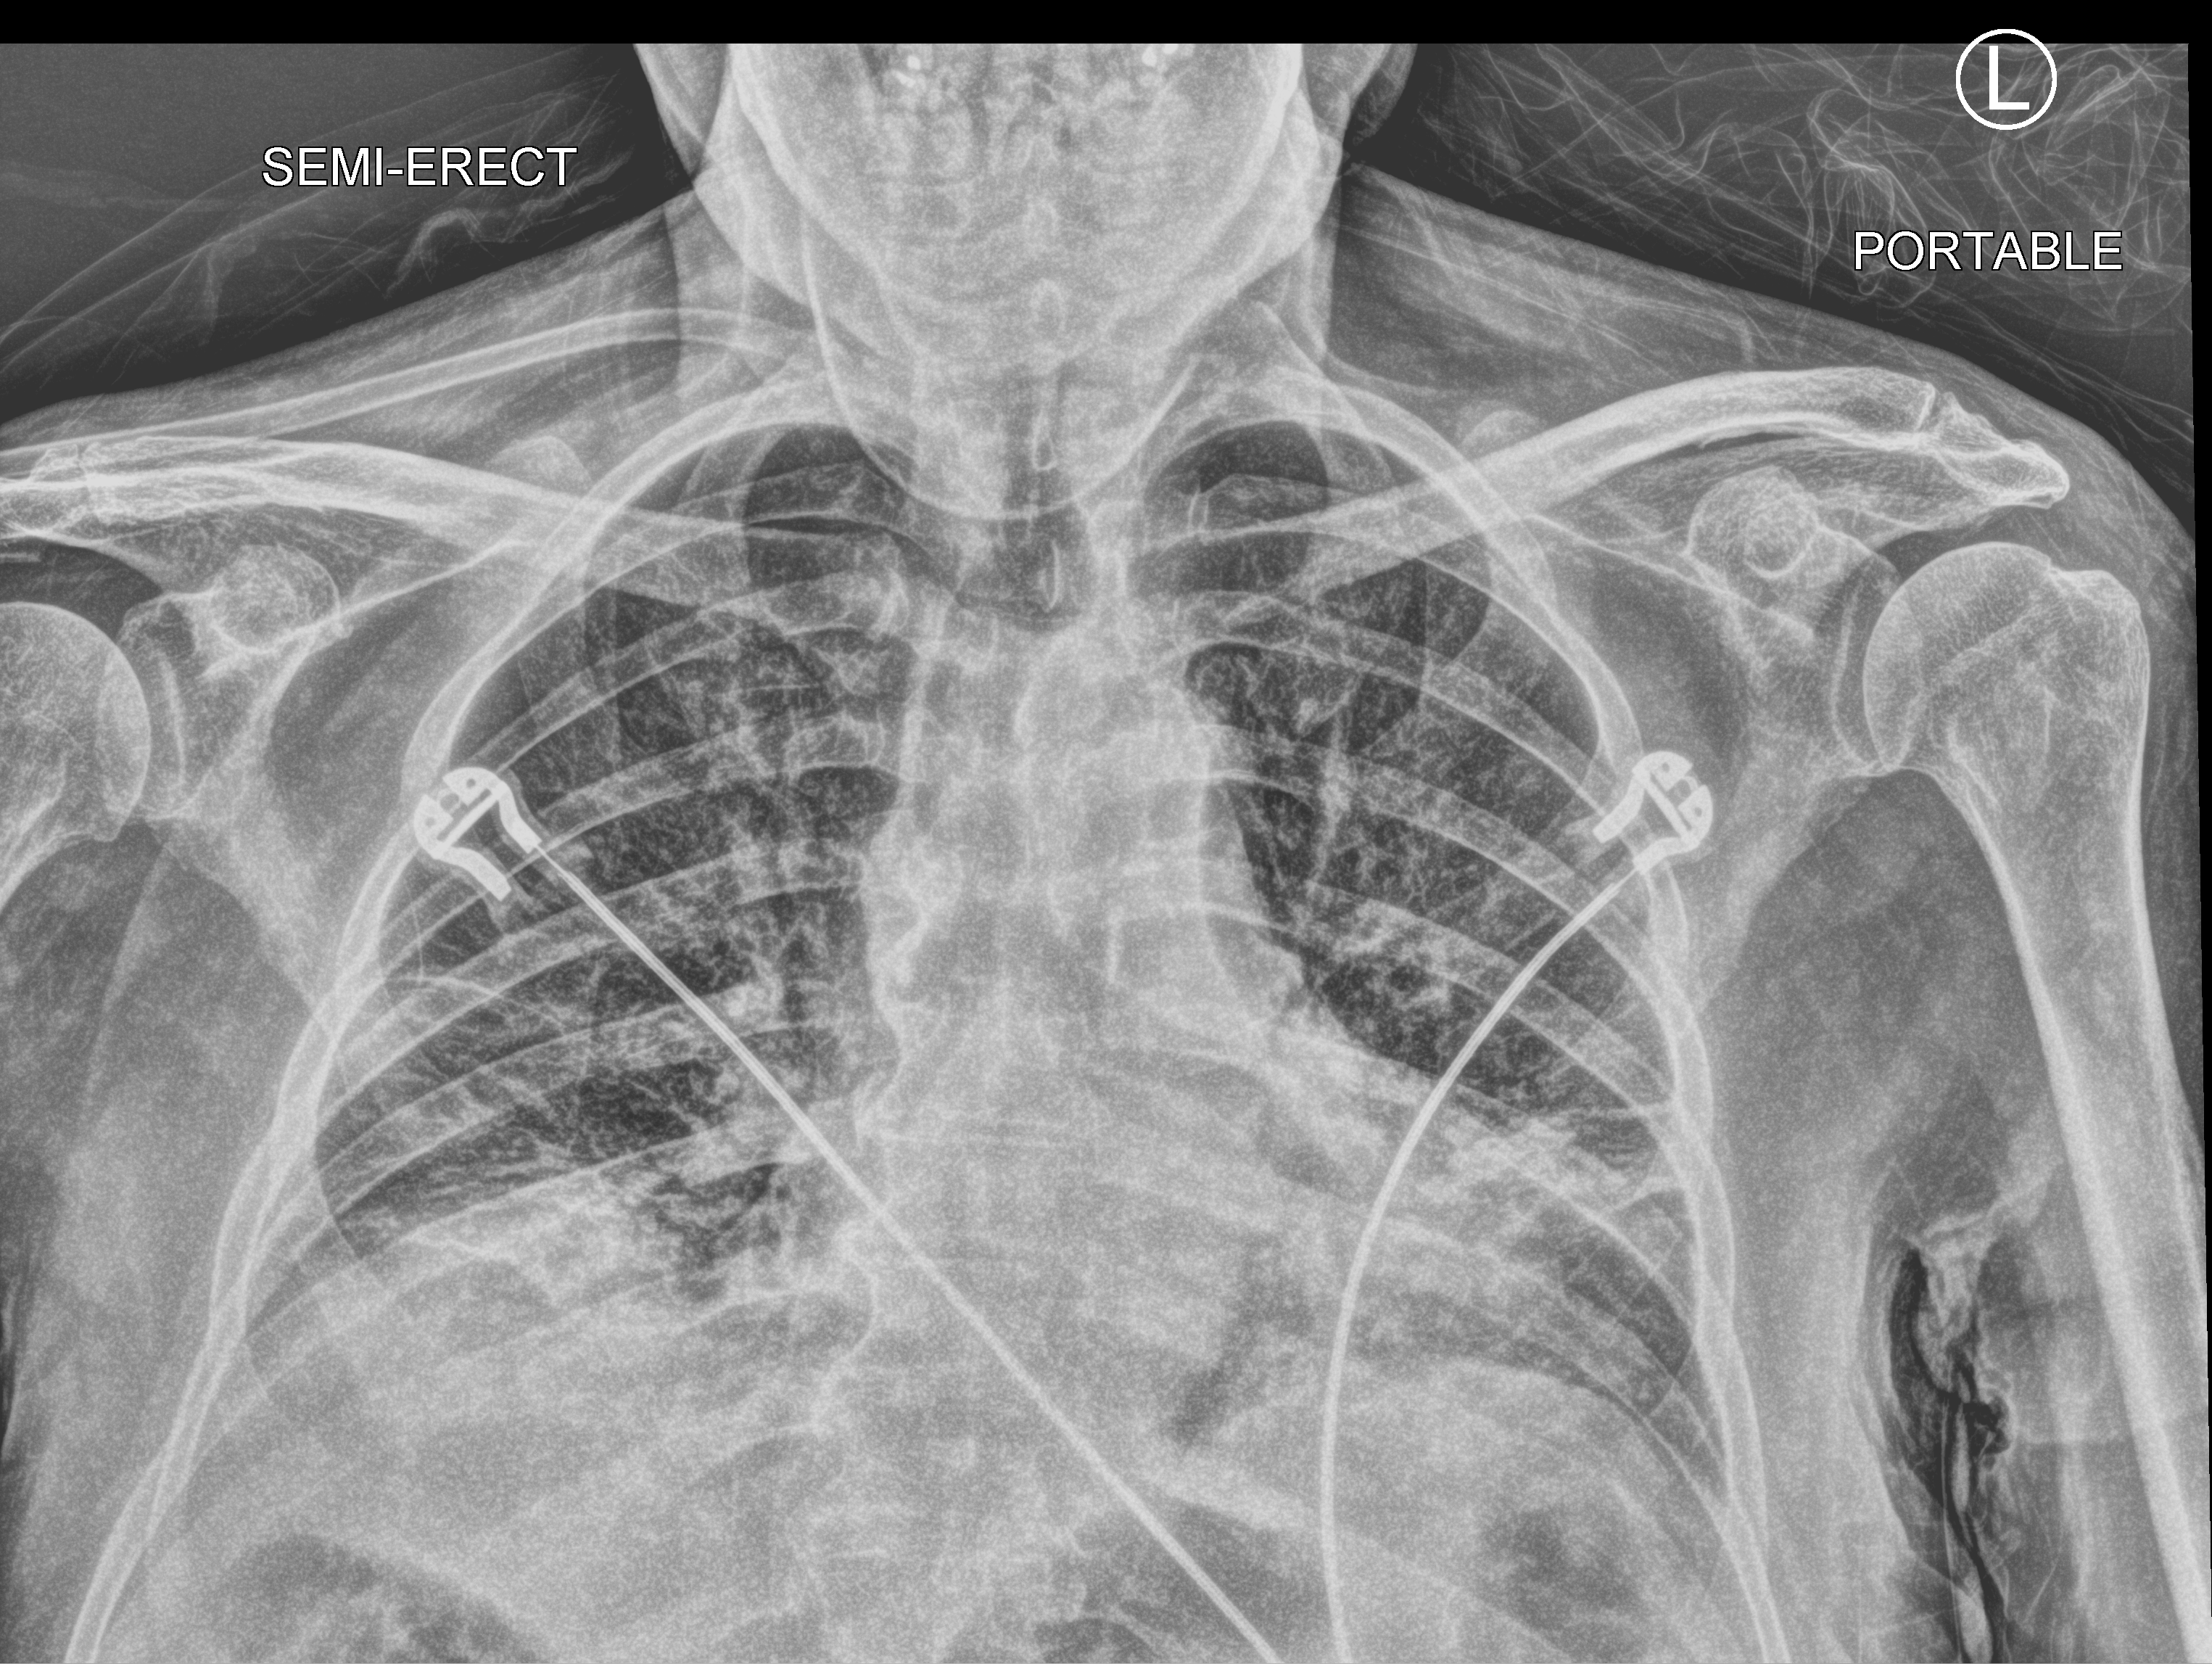
Portable chest radiograph, anteroposterior (AP) projection. Male patient hospitalised with COVID-19, age 75–90 years.
Hospital-stay facts (about this admission, not read from this image; timing relative to this image not recorded): admitted to intensive care during this hospital stay: yes; mechanically ventilated during this hospital stay: yes; length of hospital stay: 23 days.